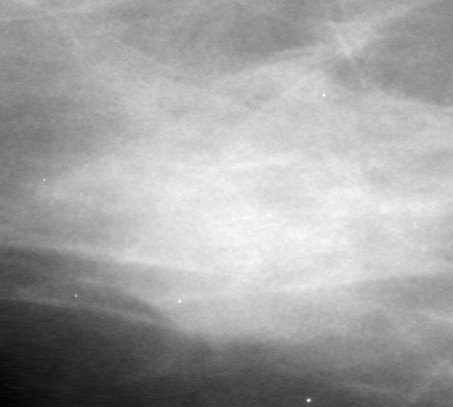
Crop from a digitized film mammogram around one marked abnormality, right breast, MLO view, BI-RADS breast density category 2 (scale 1–4).
Marked abnormality: mass, shape oval, margins obscured; BI-RADS assessment category 0 (incomplete: needs additional imaging); pathology result (as recorded, not read from the image): benign.